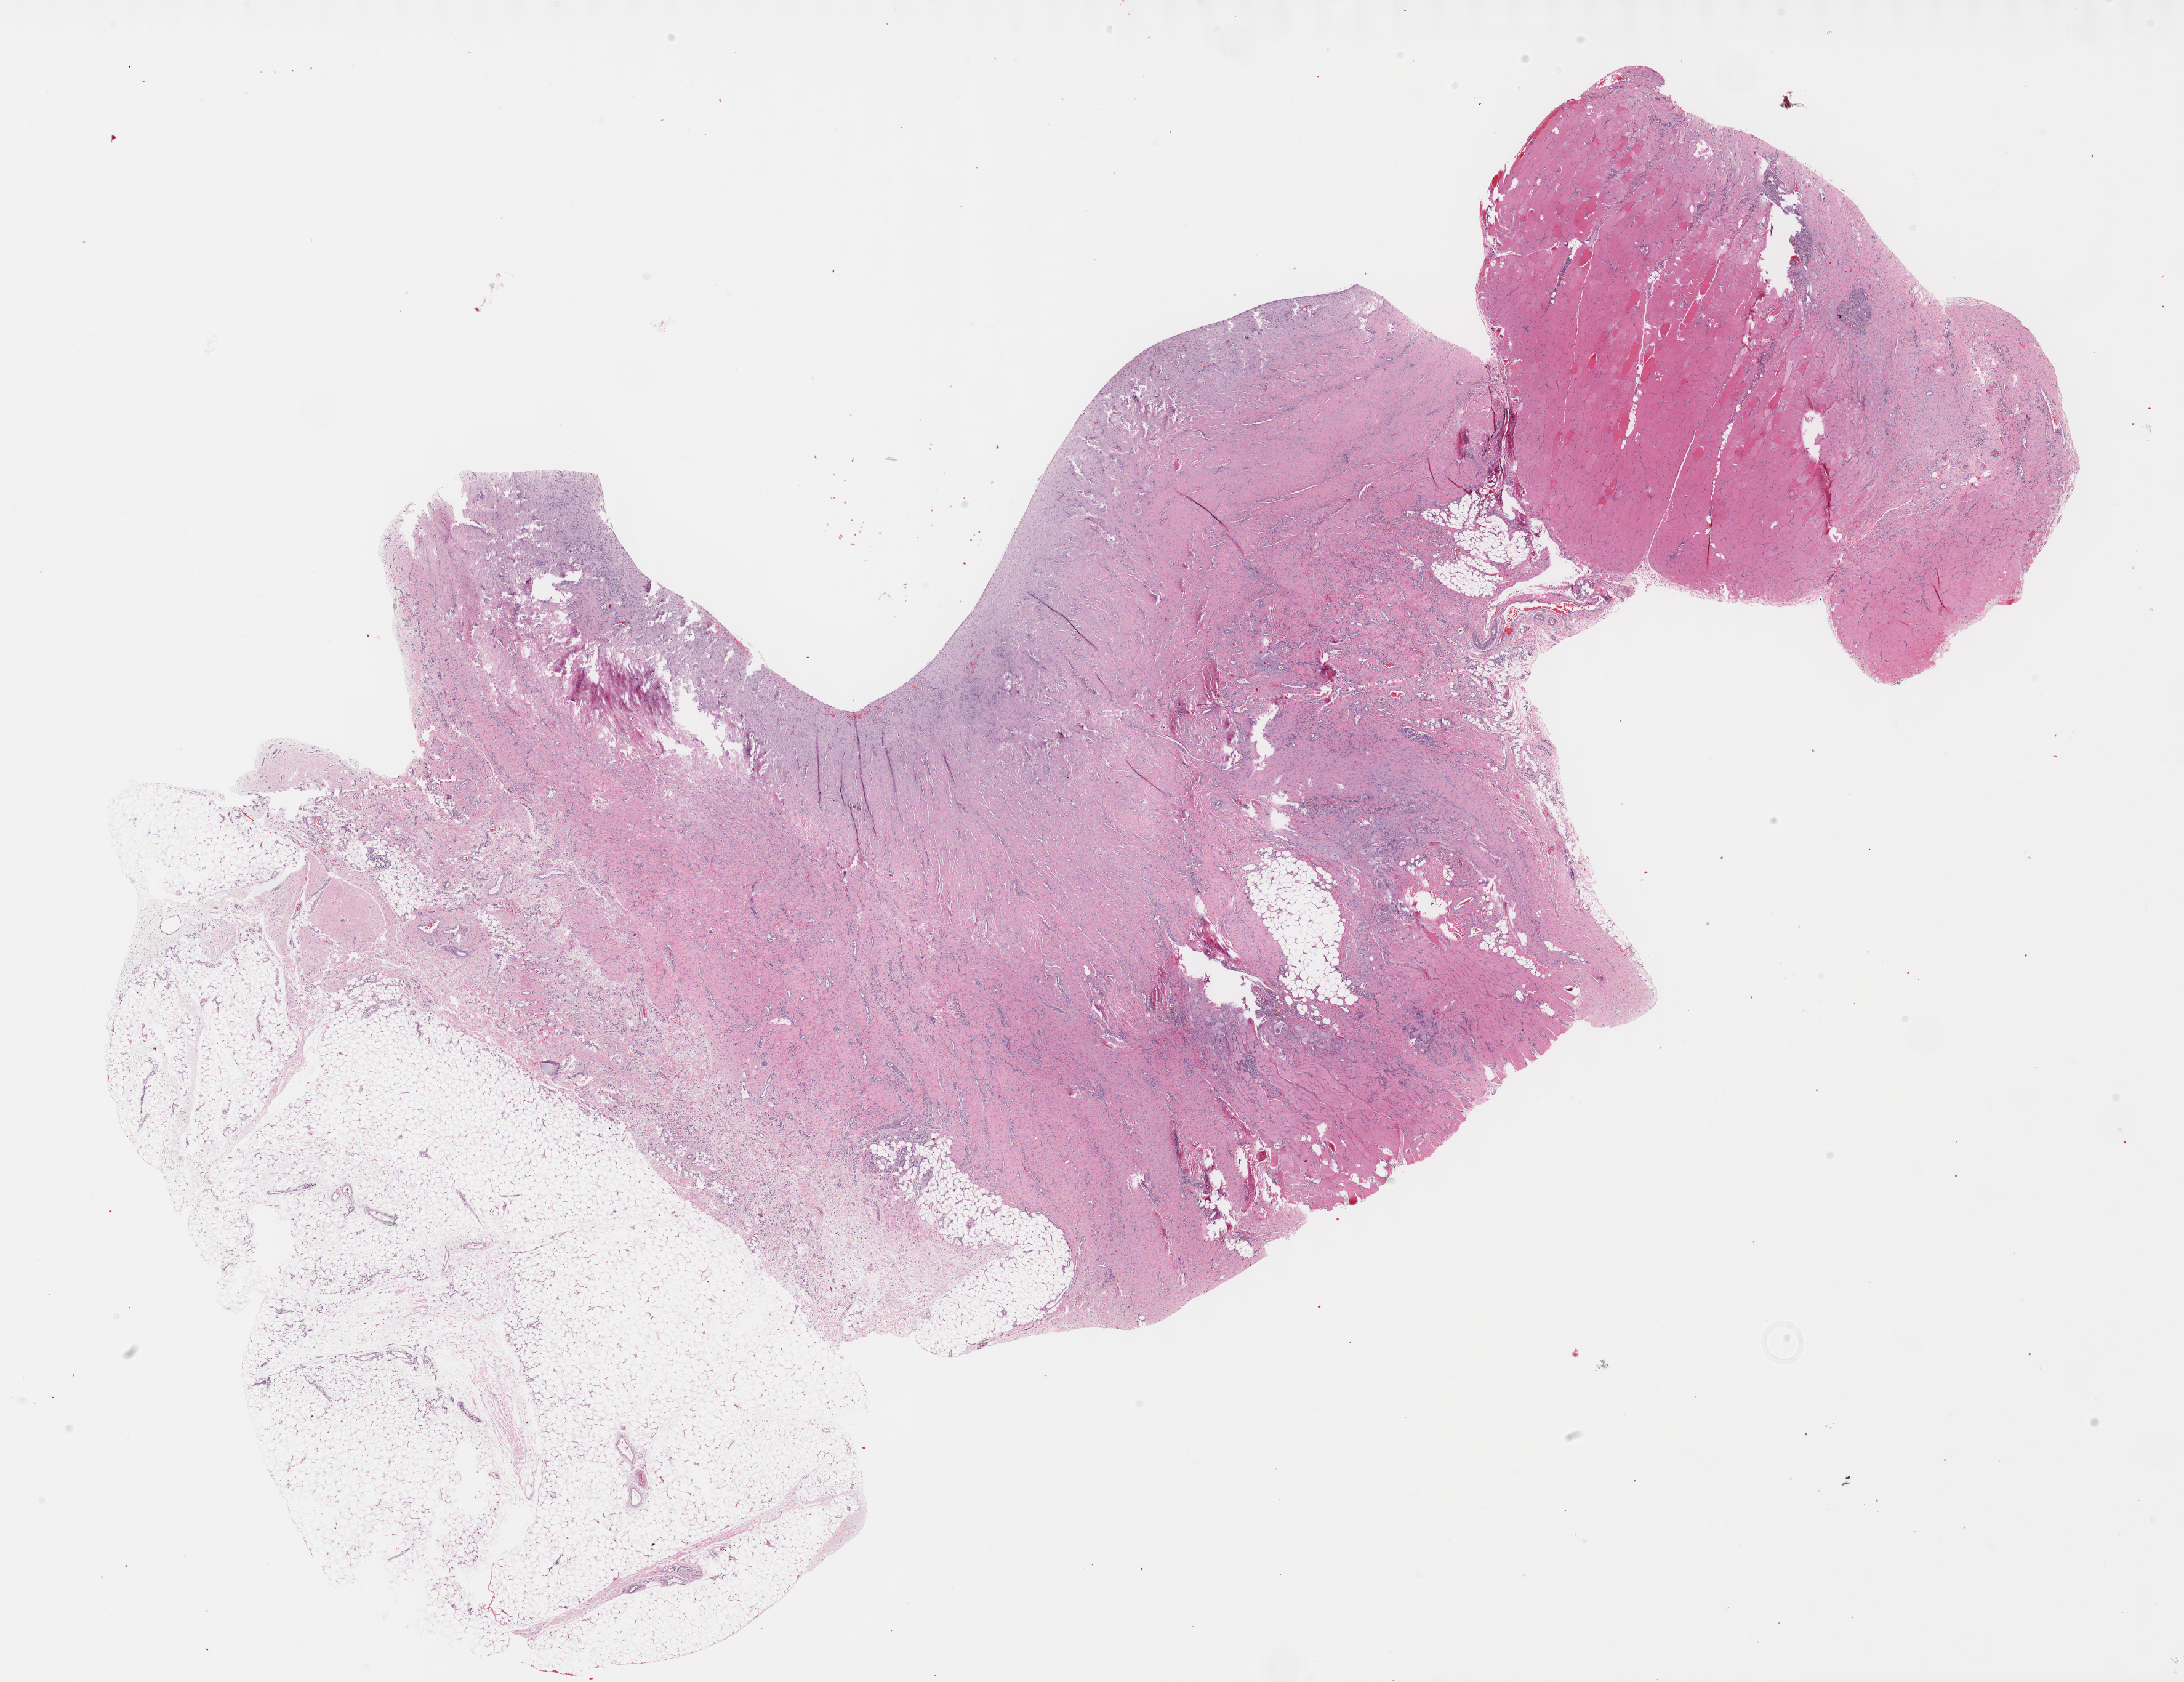
Digitized H&E tissue section (whole slide), a low-resolution overview of the entire scanned area, about 28.7 x 22.1 mm, formalin-fixed paraffin-embedded (FFPE) diagnostic section, connective, subcutaneous and other soft tissues, primary tumour sample. Male, age 35 years at initial diagnosis.
Pathologic diagnosis: Fibromyxosarcoma (connective, subcutaneous and other soft tissues of lower limb and hip).